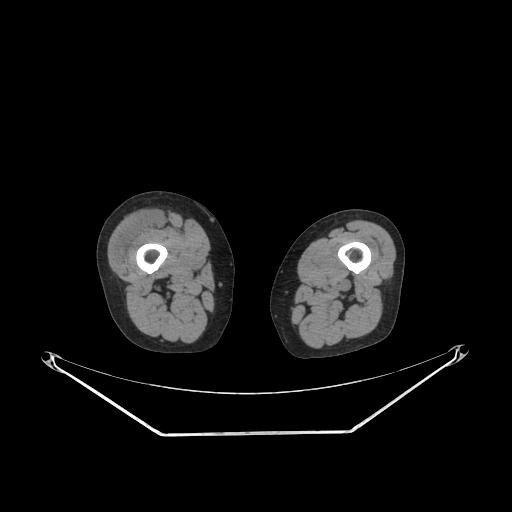
CT of an extremity soft-tissue mass (from a PET/CT study), one axial slice; slice 211 of 311 in the series (ordered by position); soft-tissue window (W 400 / L 40 HU); 3.75 mm slice thickness; 512 × 512 image matrix. Female patient. From the clinical record (not read from this slice): histological type: pleiomorphic undifferentiated sarcoma; grade: high; site of the primary tumour: right quadricep.
Annotated regions visible in this slice (expert contour drawn on MRI and transferred to this co-registered scan by the dataset authors):
- tumour plus oedema (research contour): bounding box <112,212,161,264> (left, top, right, bottom; pixels)